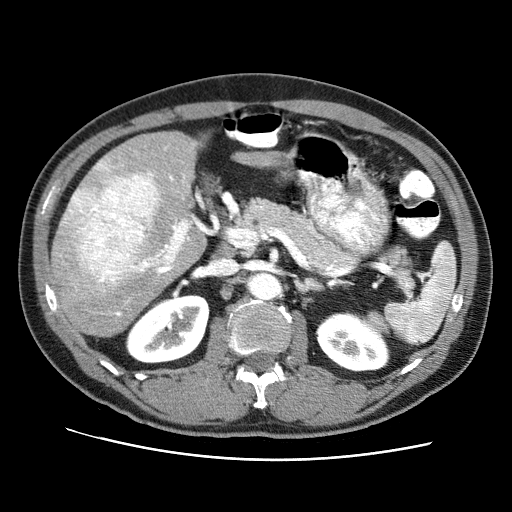
Contrast-enhanced abdominal CT (liver protocol), one axial slice; position 40 of 71 along the scan axis; reconstruction kernel STANDARD; 120 kVp; soft-tissue window (W 400 / L 40 HU); 2.5 mm slice thickness; 512 × 512 image matrix. From the clinical record (not read from this slice): diagnosis: hepatocellular carcinoma (patient treated with transarterial chemoembolisation; whether this scan precedes or follows treatment is not stated here); TNM stage (as recorded): Stage-II; Child-Pugh class: A; tumour differentiation: well differentiated; tumour size: 4.6 cm.
Structures marked on this image (semi-automatically segmented with operator editing):
- liver parenchyma outside the tumour (the mass and vessels are separate outlines, so this box may not span the whole liver): box from (x=52, y=132) to (x=281, y=336) px
- mass: (x=56, y=171)–(x=160, y=301)
- liver vessels: (x=96, y=161)–(x=196, y=316)